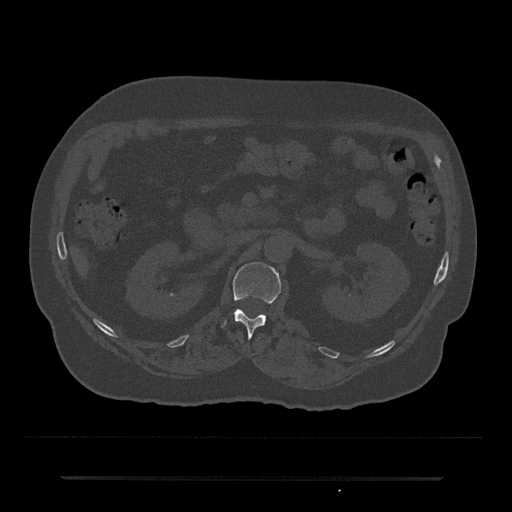
CT including the spine, one axial slice; position 66 of 797 along the scan axis; reconstruction kernel Br40s/3; bone window (W 1800 / L 400 HU); 0.5 mm slice thickness; 512 × 512 image matrix, field of view 437 × 437 mm. Male patient, age 69 years. Case-level facts recorded for this patient, not image findings: primary cancer: prostate.
Structures marked on this image (semi-automatically segmented with operator editing):
- L1 vertebra: box from (x=221, y=262) to (x=281, y=338) px